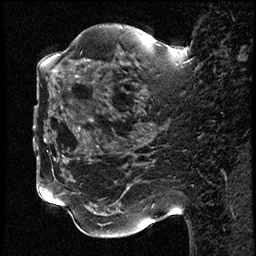
Breast MRI (dynamic contrast-enhanced), one sagittal slice; position 28 of 78 along the scan axis; dynamic contrast-enhanced study with each time point stored as its own series, time point 2 of 3 at this slice position (early post-contrast, ordered by acquisition time); 1.5 T; TE 4.2 ms, TR 17.6 ms; 2 mm slice thickness; 256 × 256 image matrix, field of view 200 × 200 mm. Female patient, age 42 years. Case-level facts recorded for this patient, not image findings: setting: breast cancer imaged before/during neoadjuvant chemotherapy; receptor status: HER2-positive.
Annotated regions visible in this slice (semi-automatically segmented with operator editing):
- analysis volume of interest (the breast-tissue region the enhancement analysis was run in; not a lesion): bounding box [x1, y1, x2, y2] px = [50, 48, 131, 129]
- tumour enhancement mask (voxels above the 100 % enhancement threshold inside the analysis volume of interest): [53, 70, 55, 72]